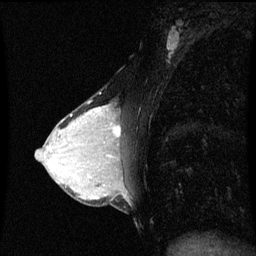
Breast MRI (dynamic contrast-enhanced), one sagittal slice. Position 33 of 60 along the scan axis. Dynamic contrast-enhanced series, image 2 of 3 at this slice position (ordered by acquisition). 1.5 T. TE 4.2 ms, TR 8.9 ms. 256 × 256 image matrix, field of view 200 × 200 mm. Patient: female, 33 years. Case-level facts recorded for this patient, not image findings: setting: breast cancer imaged before/during neoadjuvant chemotherapy; receptor status: HER2-positive.
Structures marked on this image (semi-automatically segmented with operator editing):
- analysis volume of interest (the breast-tissue region the enhancement analysis was run in; not a lesion): bounding box [x1, y1, x2, y2] px = [95, 106, 124, 153]
- tumour enhancement mask (voxels above the 70 % enhancement threshold inside the analysis volume of interest): [112, 126, 121, 137]